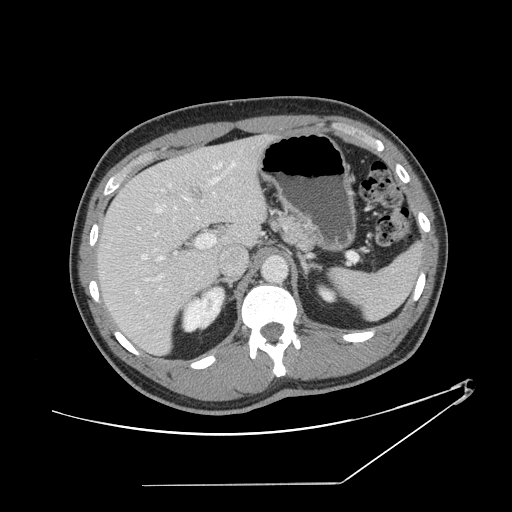
Contrast-enhanced abdominal CT, one axial slice; position 89 of 152 along the scan axis; reconstruction kernel STANDARD; 120 kVp; intravenous contrast given; soft-tissue window (W 400 / L 40 HU); 2.5 mm slice thickness; 512 × 512 image matrix, field of view 432 × 432 mm. Male patient, age 45 years. Case-level facts recorded for this patient, not image findings: diagnosis: colorectal cancer liver metastases, imaged before liver resection; multiple liver metastases: no; largest metastasis: 1 cm; disease in both lobes: no.
Structures marked on this image (outlined manually by an expert reader):
- hepatic veins: box from (x=111, y=161) to (x=223, y=294) px
- liver: (x=98, y=137)–(x=266, y=354)
- planned liver remnant (the part of the liver to remain after resection): (x=98, y=155)–(x=225, y=354)
- portal vein (with intrahepatic branches): (x=137, y=162)–(x=236, y=317)